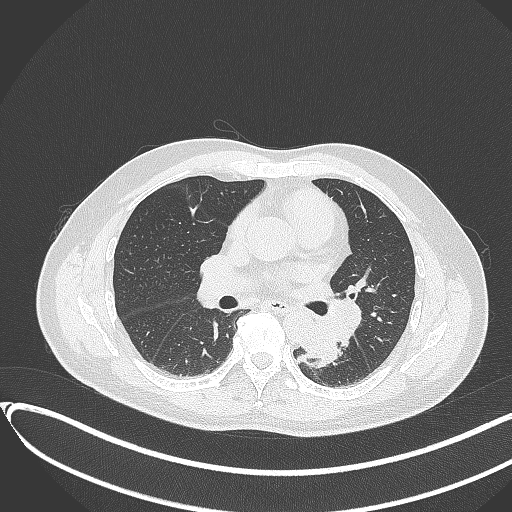
Chest CT, one axial slice; slice 185 of 417 in the series (ordered by position); reconstruction kernel B70f; 120 kVp; lung window (W 1500 / L -600 HU); 512 × 512 image matrix. Male patient, age 54 years. Case-level facts recorded for this patient, not image findings: clinical TNM (as recorded): T3 N0 M0.
Outlined on this slice (rectangle marked by the reading radiologist):
- lung tumour (recorded histology: squamous cell carcinoma): bounding box (x1, y1, x2, y2) in pixels: (294, 314, 348, 369)